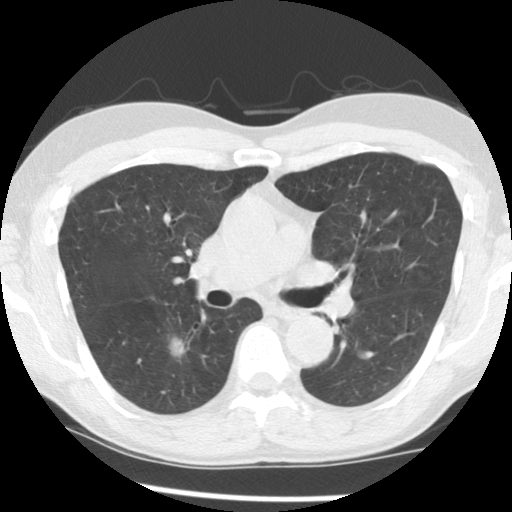
Chest CT (low-dose screening protocol), one axial image, third screening round (two years after baseline), lung window (W 1500 / L -600 HU), 2.5 mm slice thickness, standard (soft-tissue) reconstruction kernel (STANDARD), slice 83 of 145 in the series. Male participant, aged 65 years at enrolment.
- Expert-annotated lung lesion, bounding box [x1, y1, x2, y2] px = [148, 322, 210, 377].
- The screening reader recorded 2 non-calcified nodules or masses ≥4 mm on this exam; which of them this box marks is not recorded.
- Official screen result: positive, other.
- Lung cancer was diagnosed 116 days after this screen: adenocarcinoma, NOS, right lower lobe, poorly differentiated (G3), stage IA (AJCC 6th edition), 18 mm at pathology.